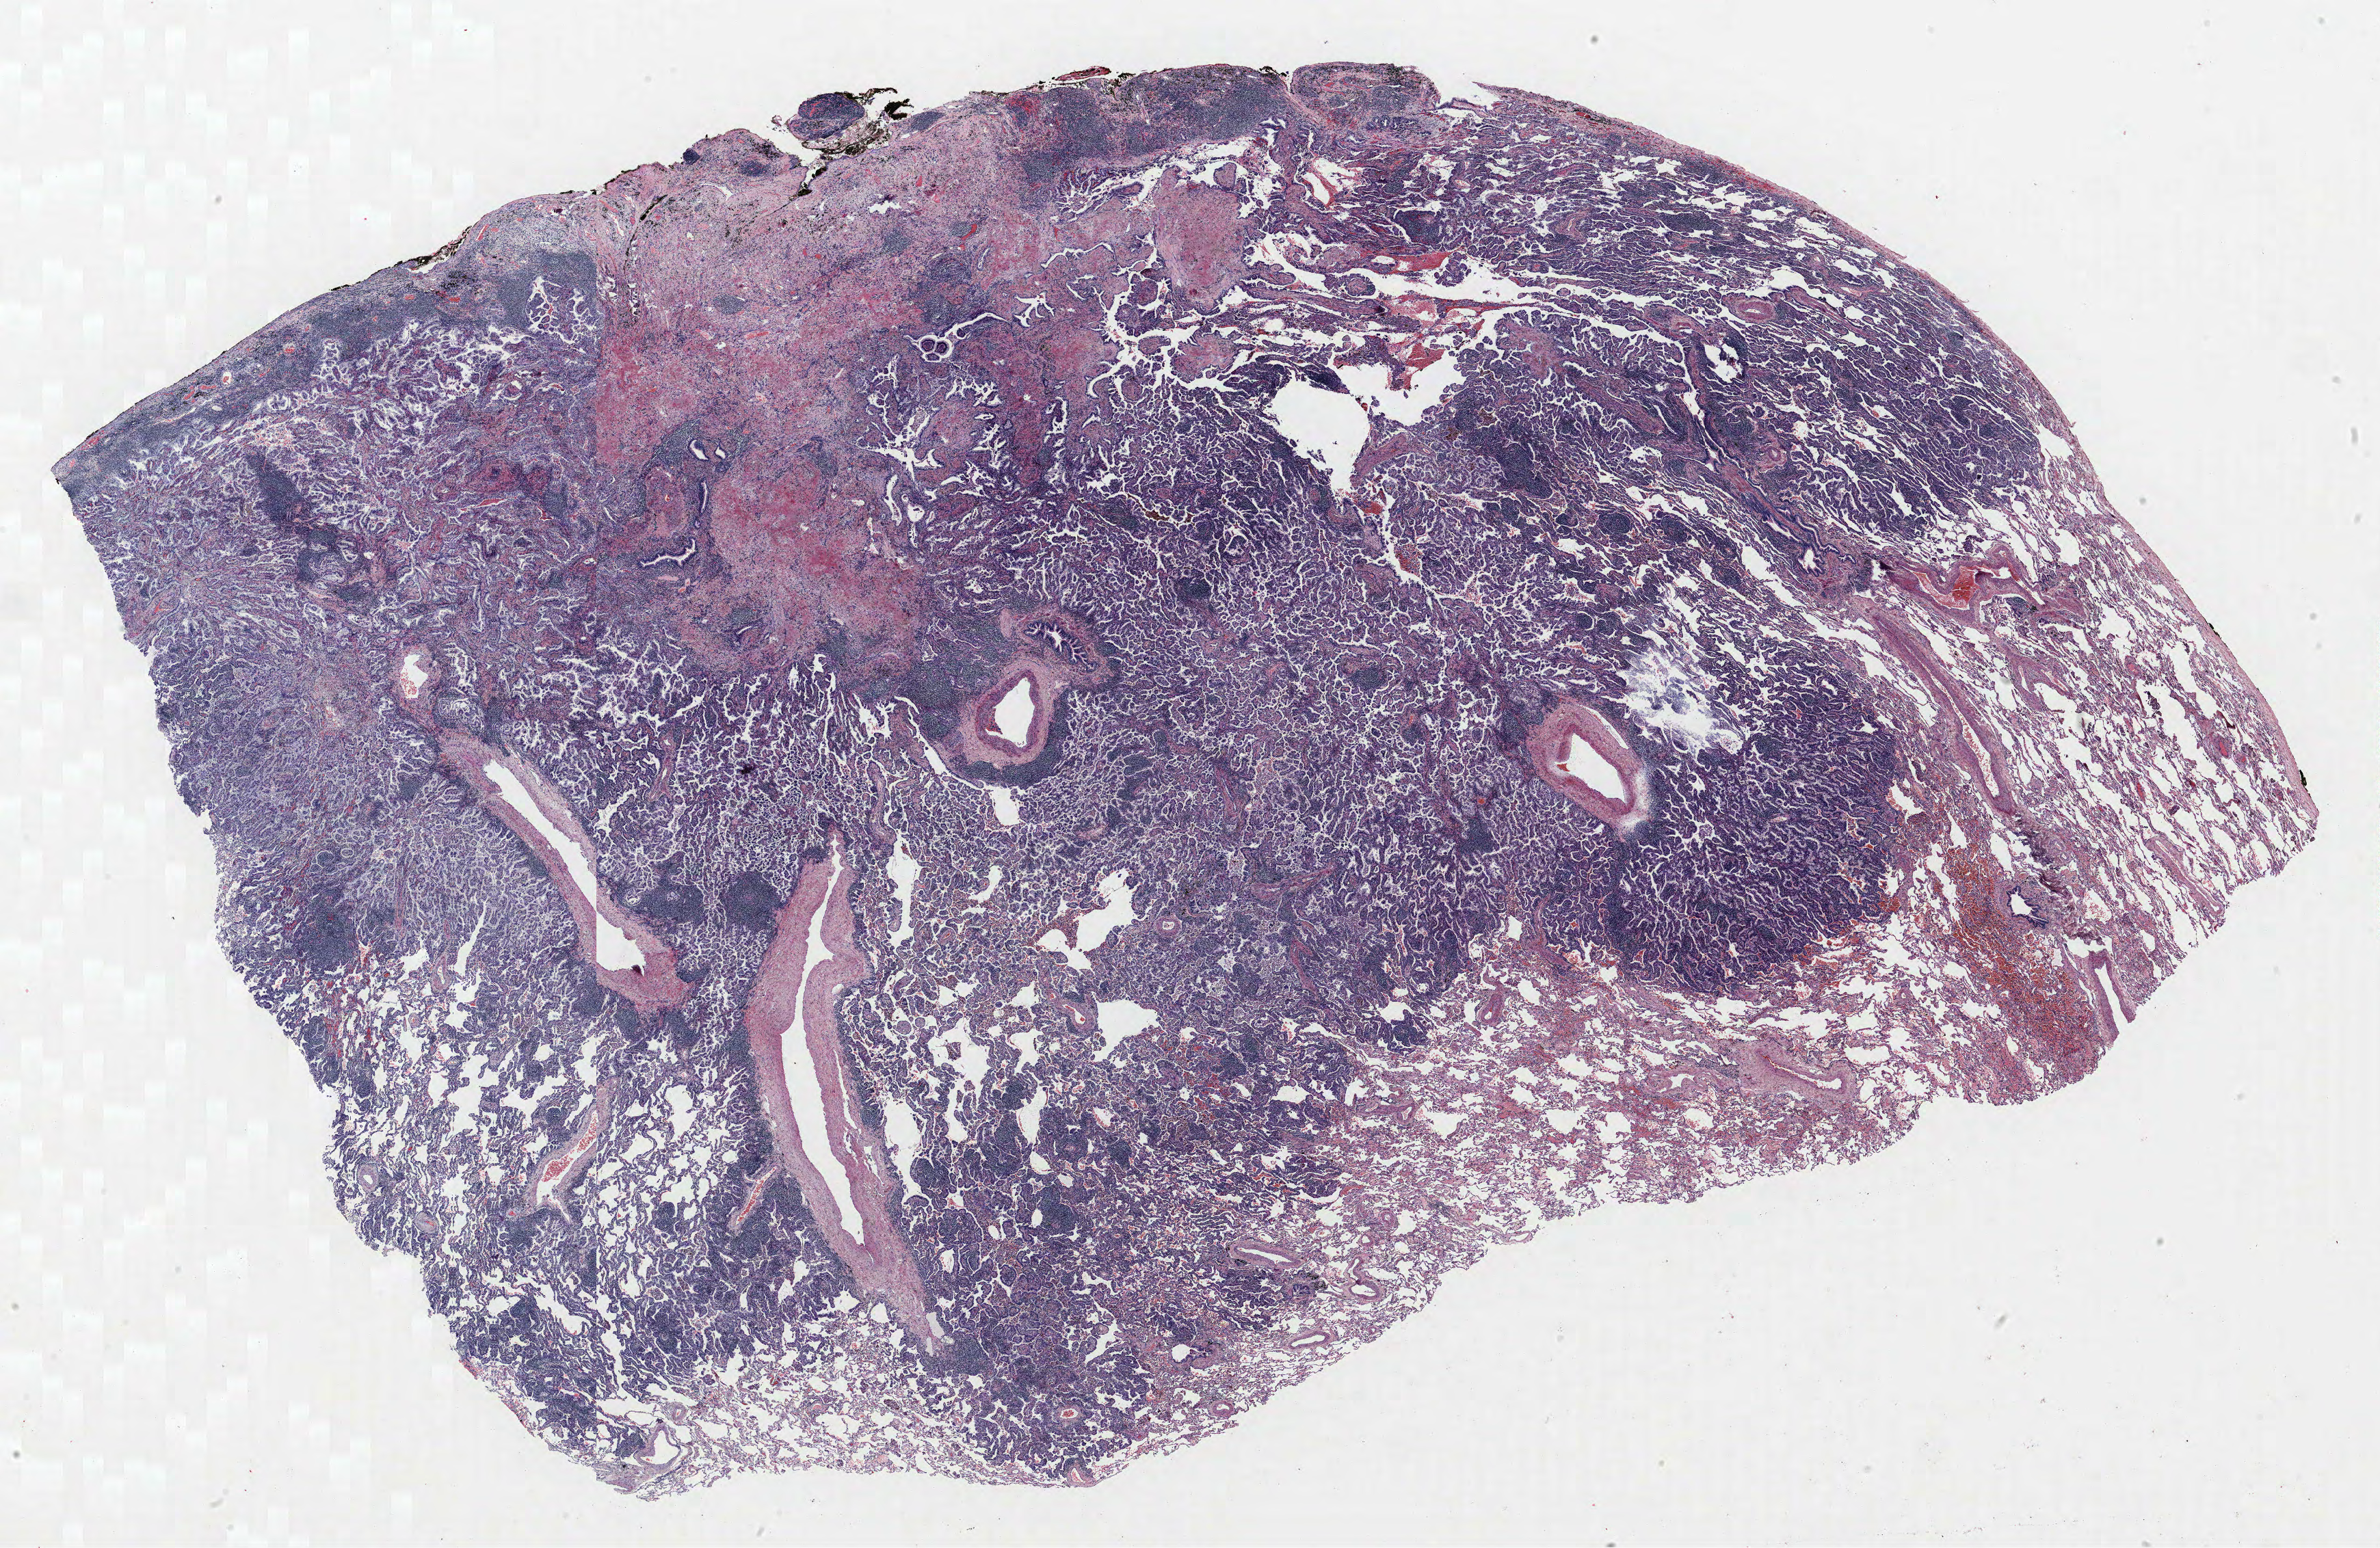
Whole-slide histology image, Hematoxylin and eosin (H&E) stained — low-resolution overview of the scanned area, about 27.8 x 18.1 mm (slide scanned at 40x); formalin-fixed paraffin-embedded (FFPE) section; lung tissue. Male, age 60 at enrolment. Current smoker at enrolment. Grade: well differentiated (G1).
• tumour size (pathology): 27 mm
• stage (AJCC 6th edition): IA
• primary tumour location (clinical record): left upper lobe
• participant's lung-cancer diagnosis: Bronchiolo-alveolar adenocarcinoma, NOS (ICD-O-3 8250/3)